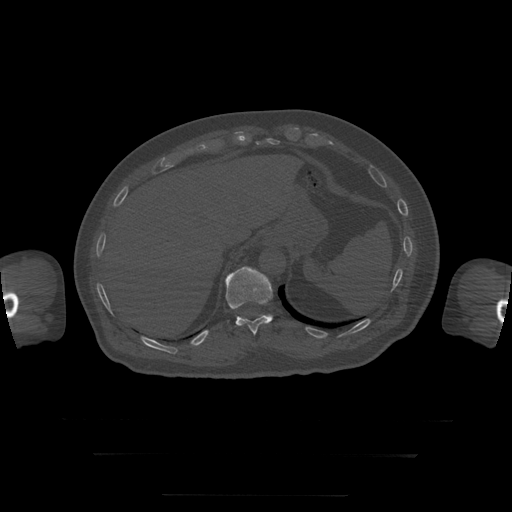
CT including the spine, one axial slice. Position 97 of 397 along the scan axis. Reconstruction kernel STANDARD. 120 kVp. Bone window (W 1800 / L 400 HU). 1.25 mm slice thickness. 512 × 512 image matrix, field of view 510 × 510 mm. Patient age 73 years. Case-level facts recorded for this patient, not image findings: primary cancer: prostate.
Outlined on this slice (semi-automatically segmented with operator editing):
- T11 vertebra: box from (x=225, y=267) to (x=273, y=335) px
- T12 vertebra: (x=266, y=315)–(x=272, y=317)